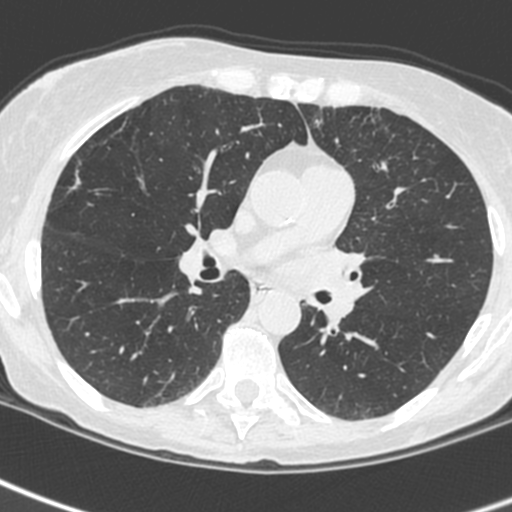
Low-dose screening chest CT, one axial slice; slice 137 of 242 in the series (ordered by position); lung window (W 1500 / L -600 HU); 512 × 512 image matrix, field of view 284 × 284 mm.
Annotated regions visible in this slice (outlined manually by an expert reader):
- lesion 3 (tumor, upper lobe of left lung): bounding box [x1, y1, x2, y2] px = [304, 248, 365, 330]